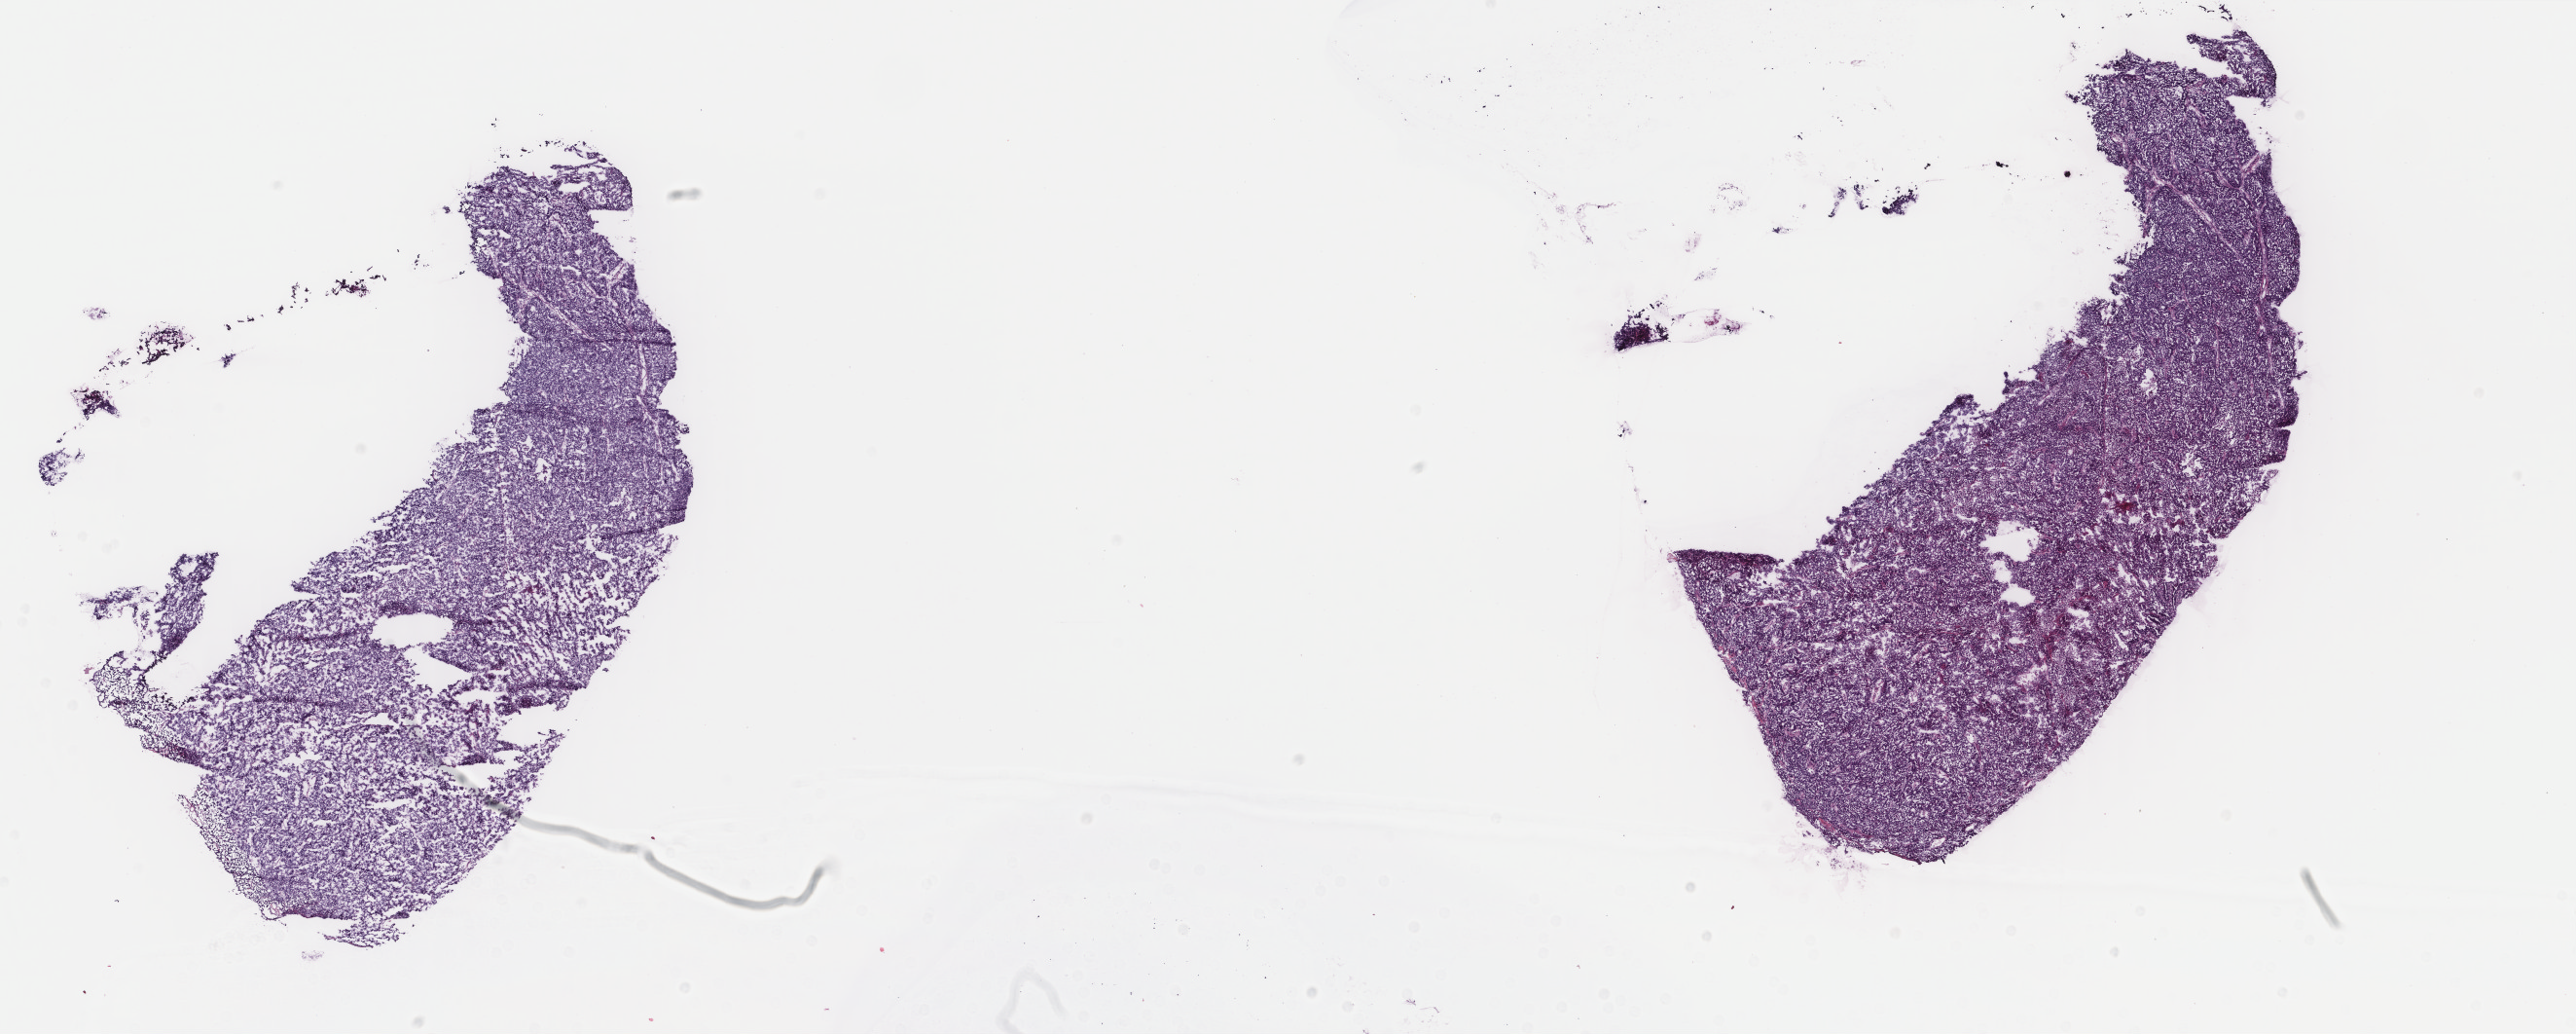
Digitized H&E tissue section (whole slide) — low-resolution overview of the scanned area, about 21.0 x 8.4 mm; frozen section from the top of the tissue portion; primary tumour sample from the uterus. Female, age 60 years at initial diagnosis. Histologic grade: G3 (poorly differentiated). Pathologist review of this section (percent, as recorded): tumour cells 96%, tumour nuclei 98%, normal cells 0%, stromal cells 2%, necrosis 2%. Inflammatory infiltration, as recorded: lymphocyte infiltration 5%, monocyte infiltration 8%, neutrophil infiltration 2%.
Diagnosis: Serous cystadenocarcinoma, NOS (endometrium). FIGO stage: IA. Lymph nodes positive (case pathology): 0 of 2 examined.